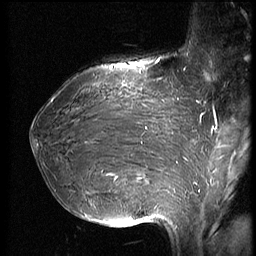
Breast MRI (dynamic contrast-enhanced), one sagittal slice. Position 26 of 66 along the scan axis. Dynamic contrast-enhanced series, image 2 of 3 at this slice position (ordered by acquisition). 1.5 T. TE 4.2 ms, TR 8.9 ms. 2.5 mm slice thickness. 256 × 256 image matrix, field of view 200 × 200 mm. Patient: female, 39 years. From the clinical record (not read from this slice): setting: breast cancer imaged before/during neoadjuvant chemotherapy; receptor status: HER2-positive.
Outlined on this slice (semi-automatic segmentation, software-assisted and operator-edited):
- analysis volume of interest (the breast-tissue region the enhancement analysis was run in; not a lesion): bounding box (x1, y1, x2, y2) in pixels: (32, 75, 188, 218)
- tumour enhancement mask (voxels above the 140 % enhancement threshold inside the analysis volume of interest): (53, 99, 151, 213)